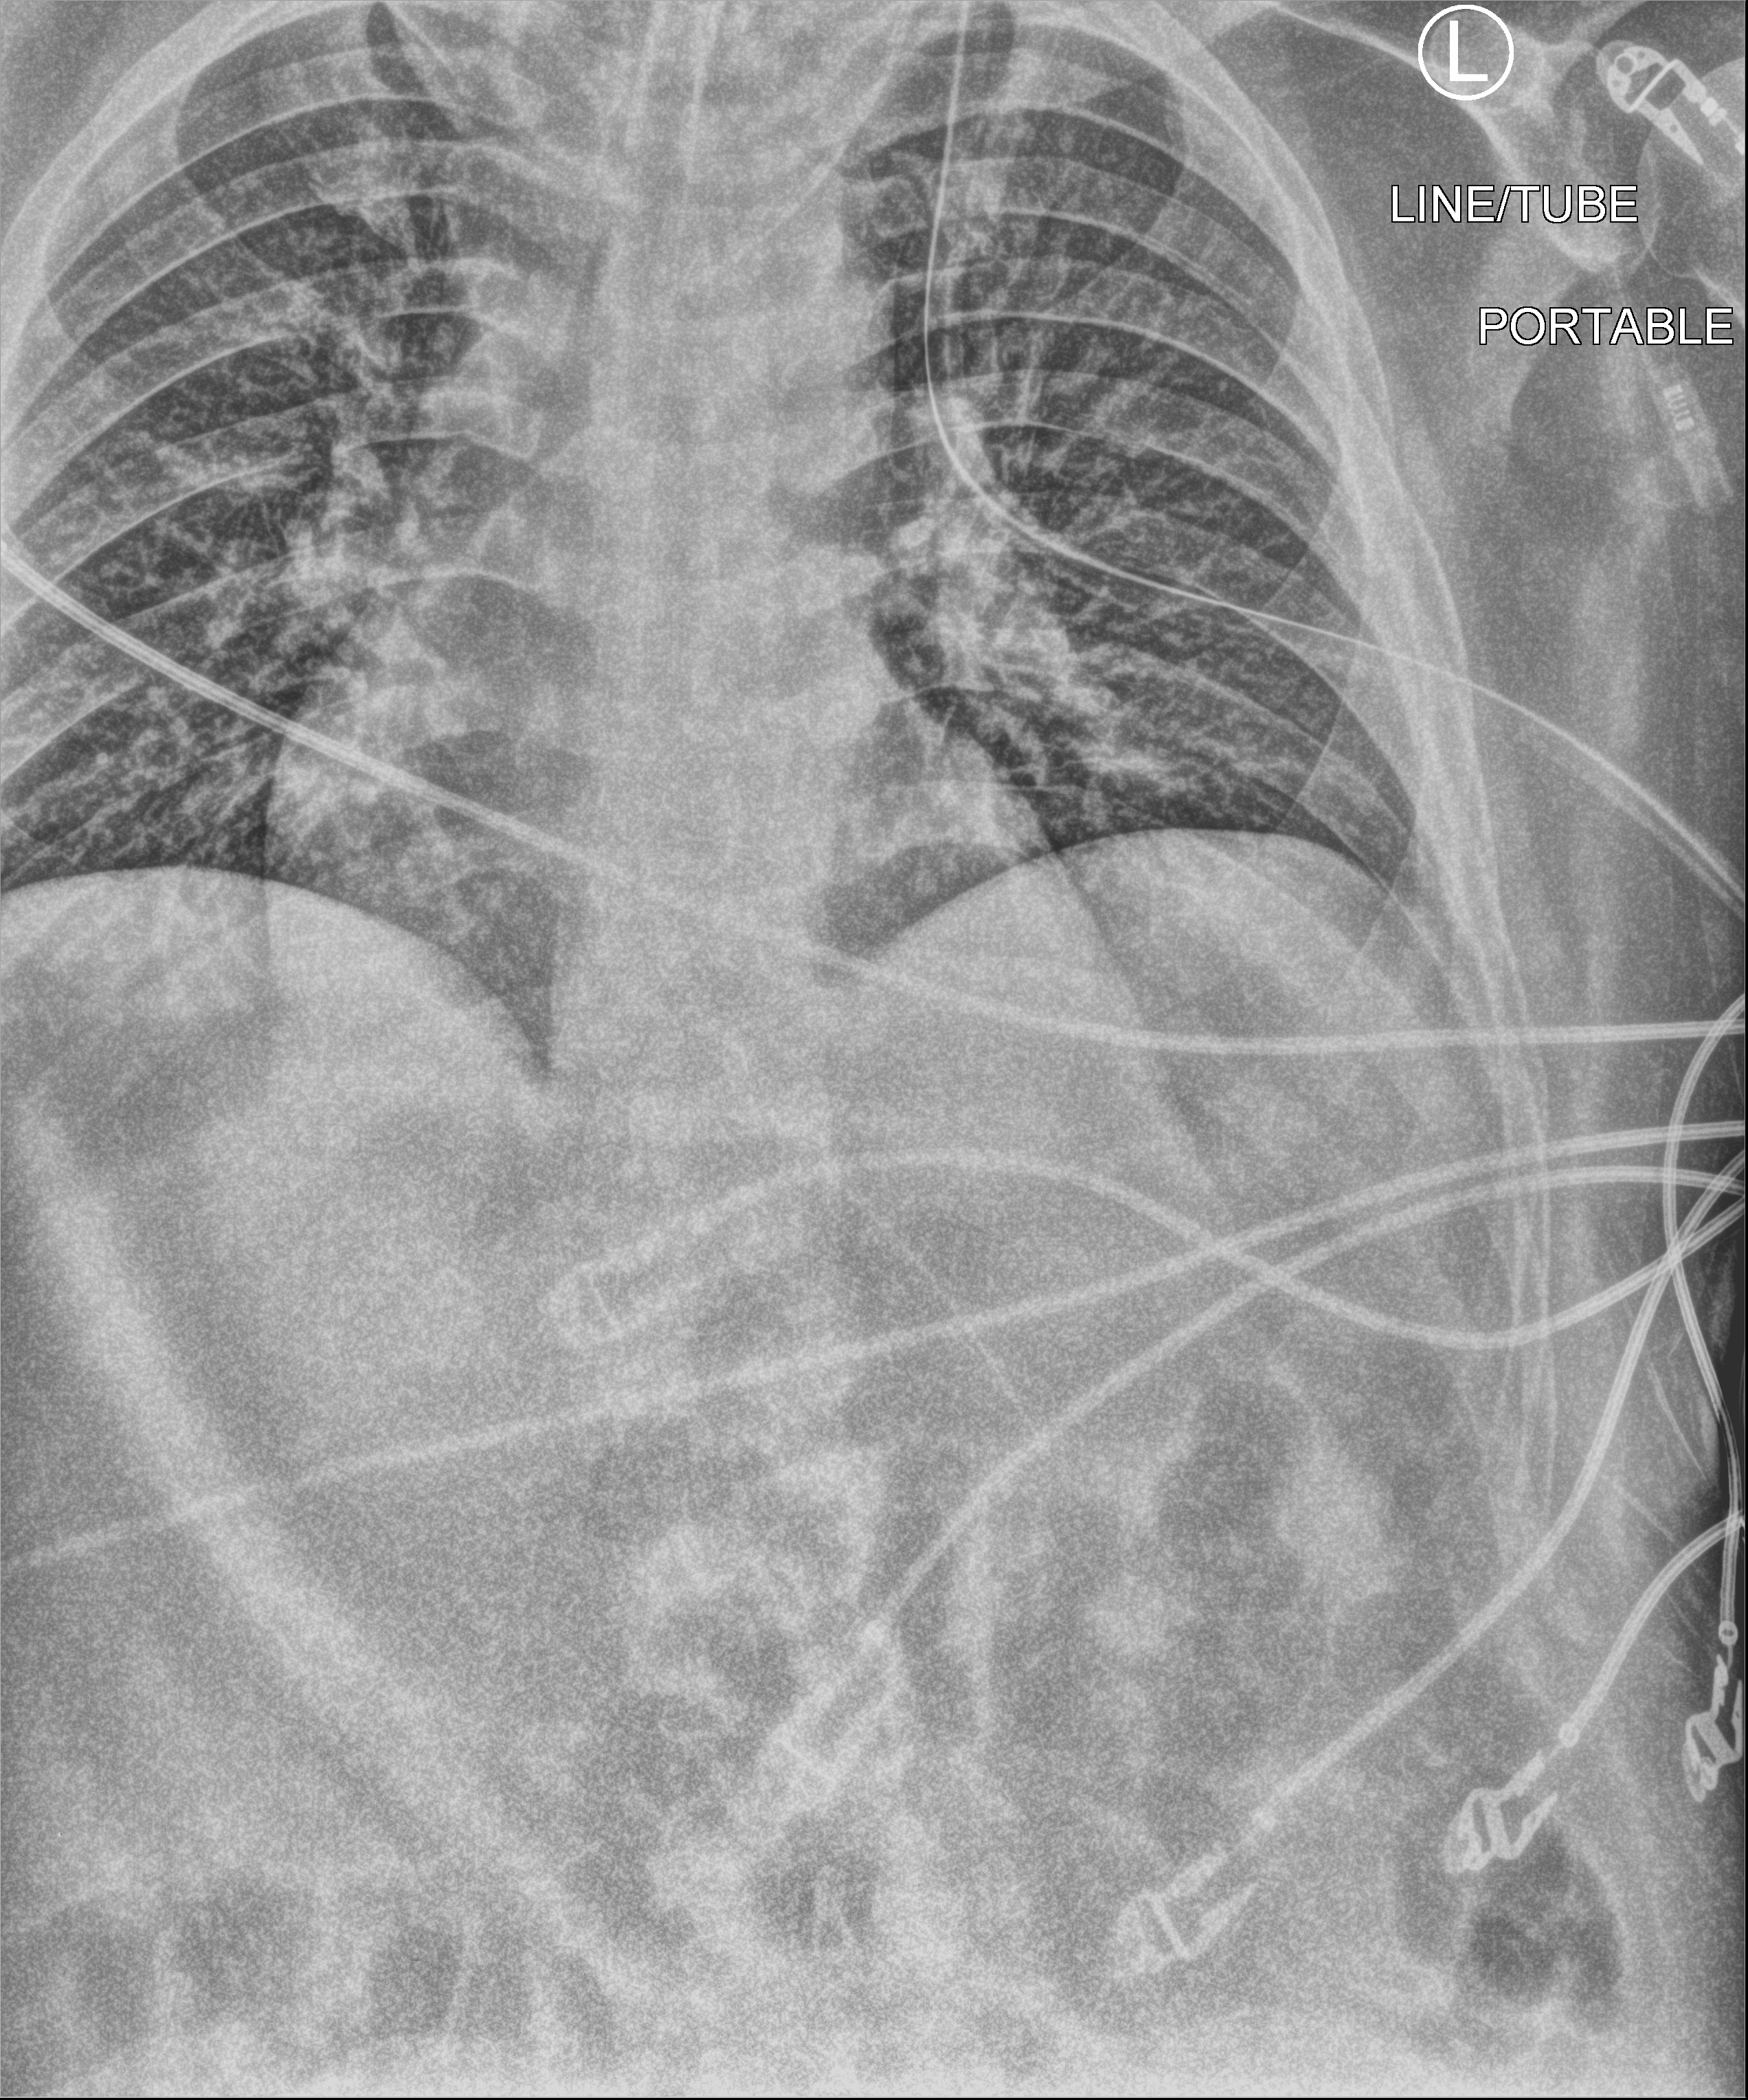
Chest X-ray (portable); anteroposterior (AP) projection. Male patient hospitalised with COVID-19, age 18–59 years.
Hospital-stay facts (about this admission, not read from this image; timing relative to this image not recorded):
- mechanically ventilated during this hospital stay: yes